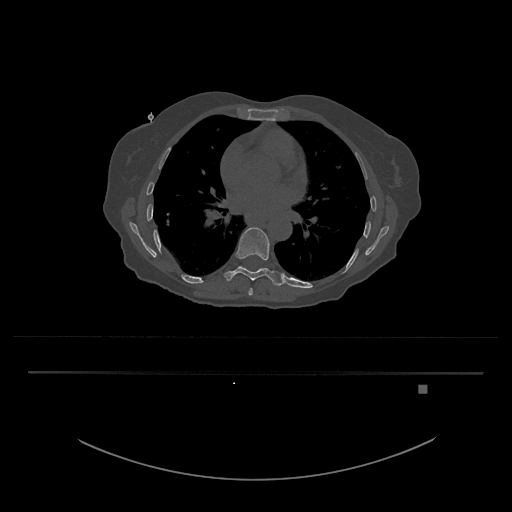
CT including the spine, one axial slice; slice 759 of 797 in the series (ordered by position); reconstruction kernel Br40s/3; 120 kVp; bone window (W 1800 / L 400 HU); 0.5 mm slice thickness; 512 × 512 image matrix, field of view 500 × 500 mm. Female patient, age 57 years. Case-level facts recorded for this patient, not image findings: primary cancer: cervical.
Structures marked on this image (semi-automatic segmentation, software-assisted and operator-edited):
- T10 vertebra: box from (x=240, y=265) to (x=264, y=272) px
- T8 vertebra: (x=248, y=288)–(x=253, y=296)
- T9 vertebra: (x=224, y=227)–(x=284, y=286)